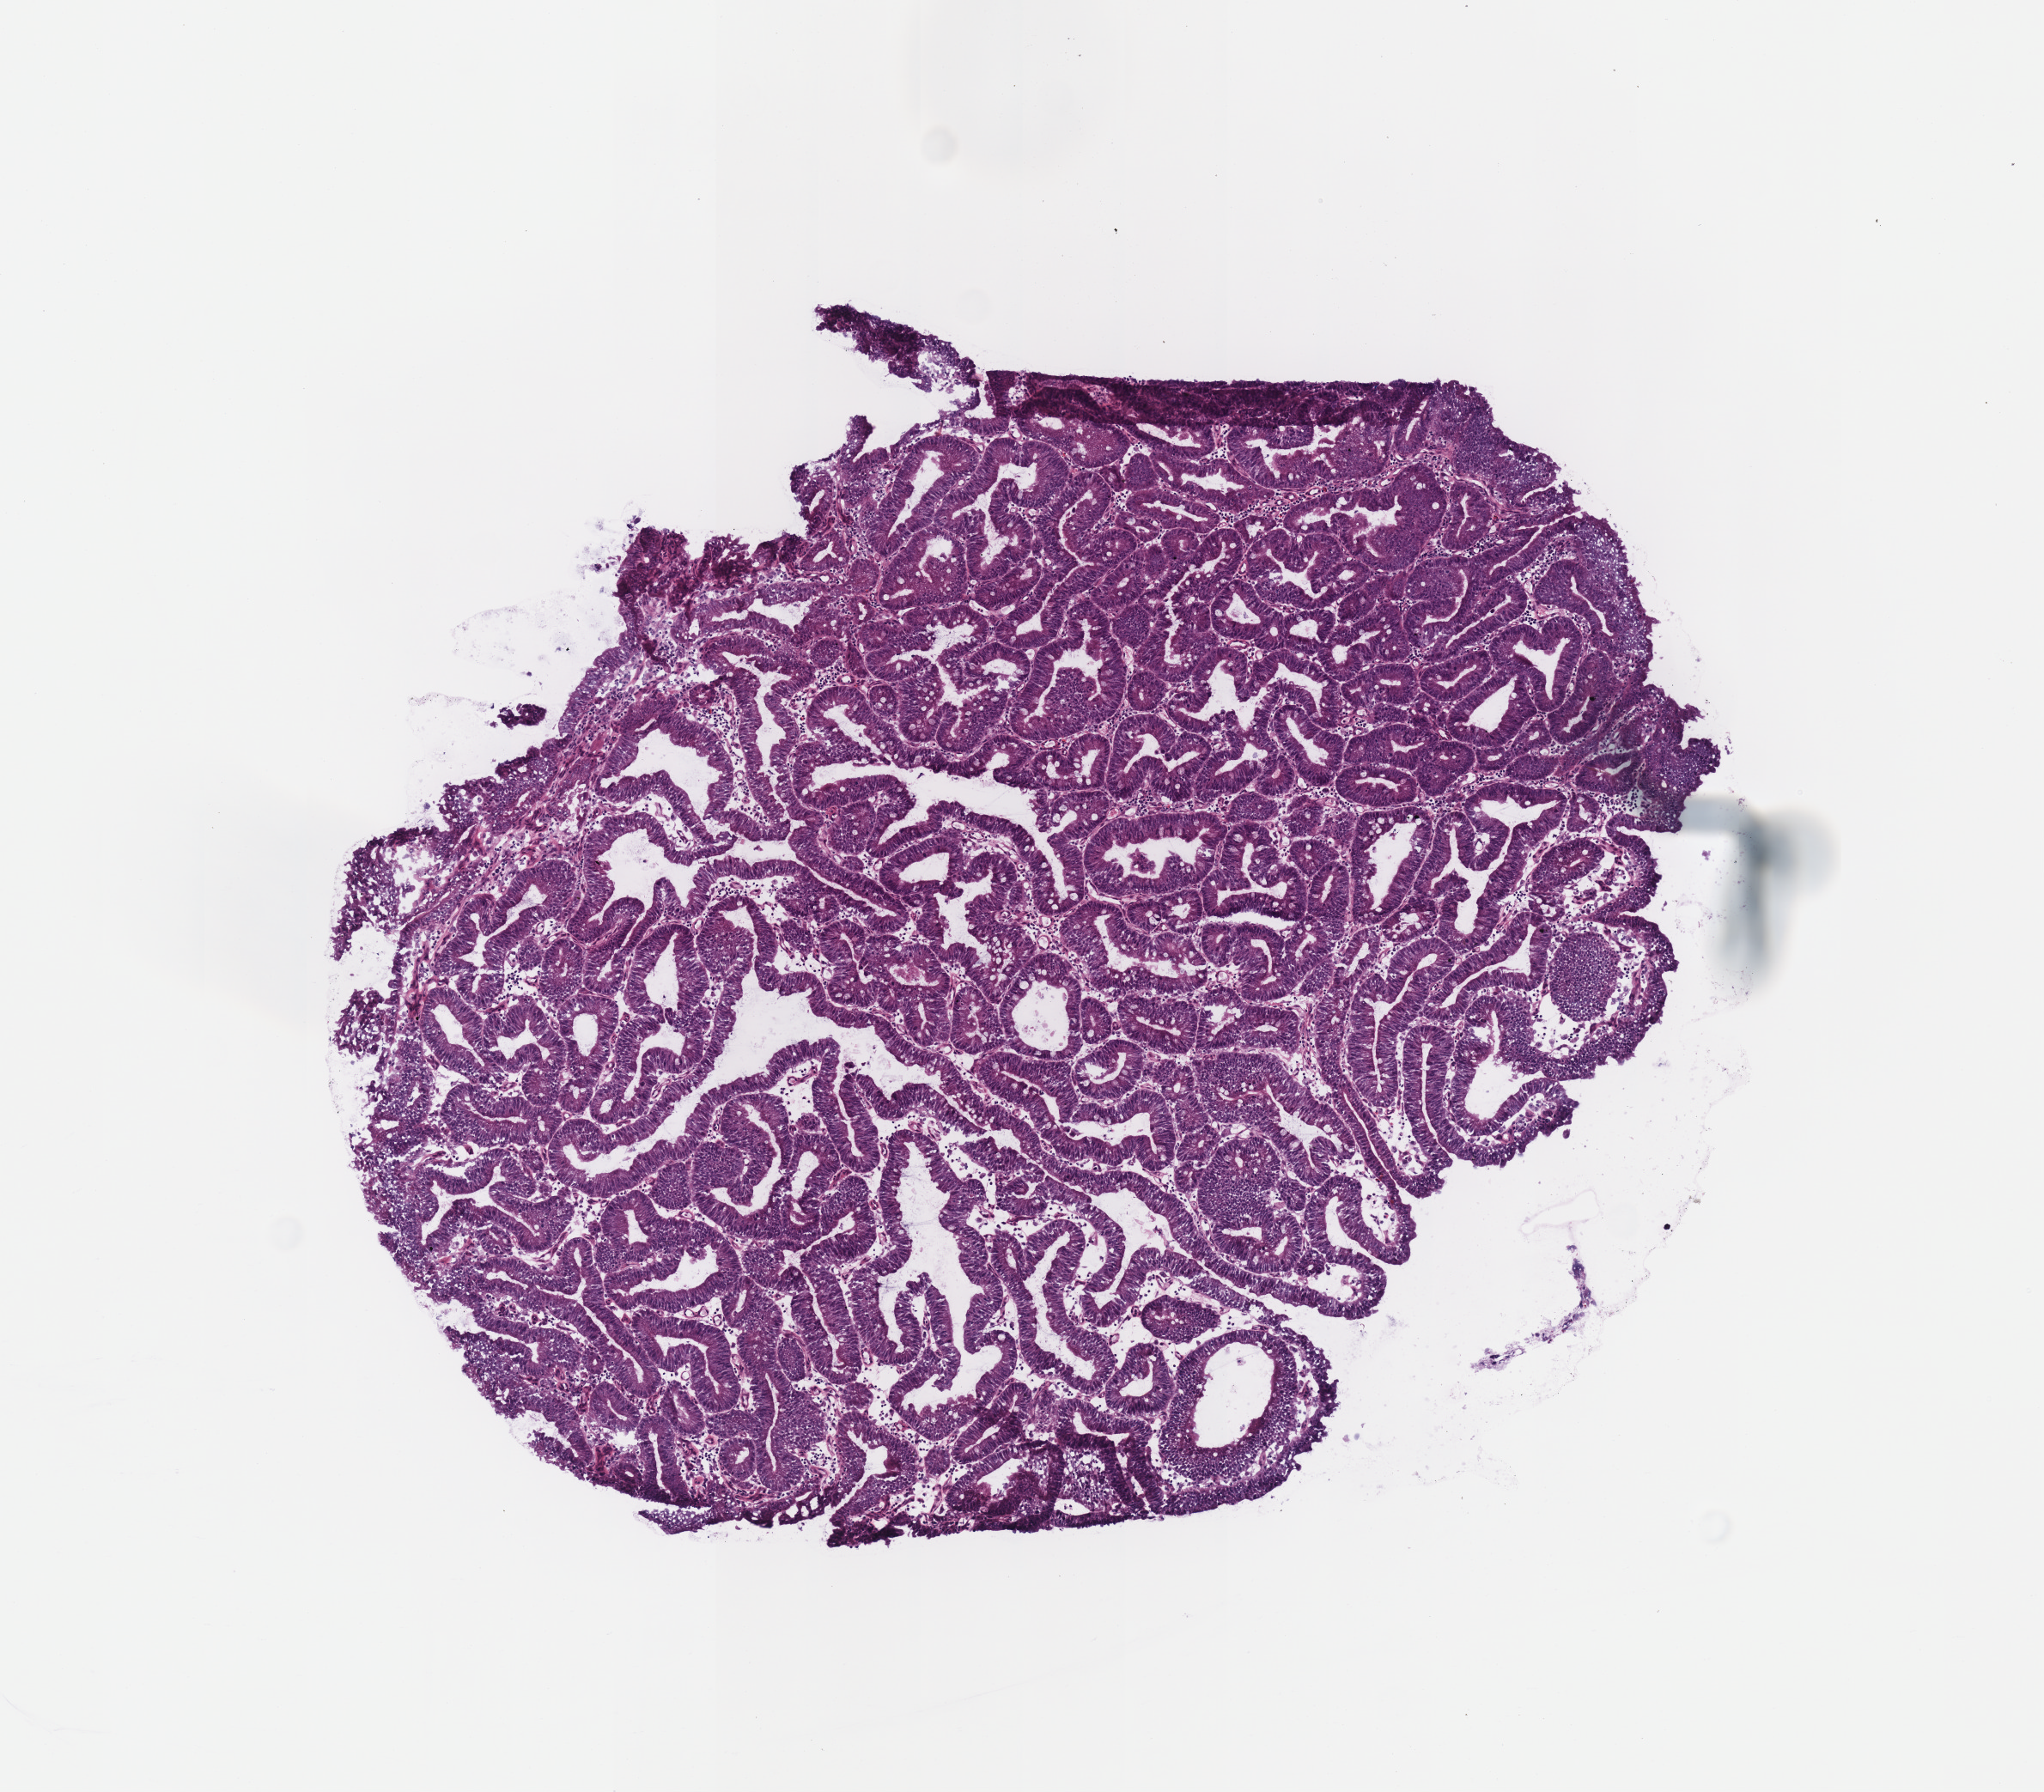
H&E-stained whole-slide image — whole scanned area (about 4.7 x 4.1 mm, from a 40x scan) shown as a low-resolution overview. Frozen section. Primary tumour sample from the stomach. Female patient; age at initial diagnosis 77 years. Histologic grade: G1 (well differentiated). Pathologist review of this section (percent, as recorded): tumour cells 90%, tumour nuclei 80%, normal cells 0%, stromal cells 10%, necrosis 0%.
* lymph nodes positive (case pathology): 0 of 32 examined
* AJCC pathologic stage: IA (7th edition)
* pathologic diagnosis: Tubular adenocarcinoma (body of stomach)